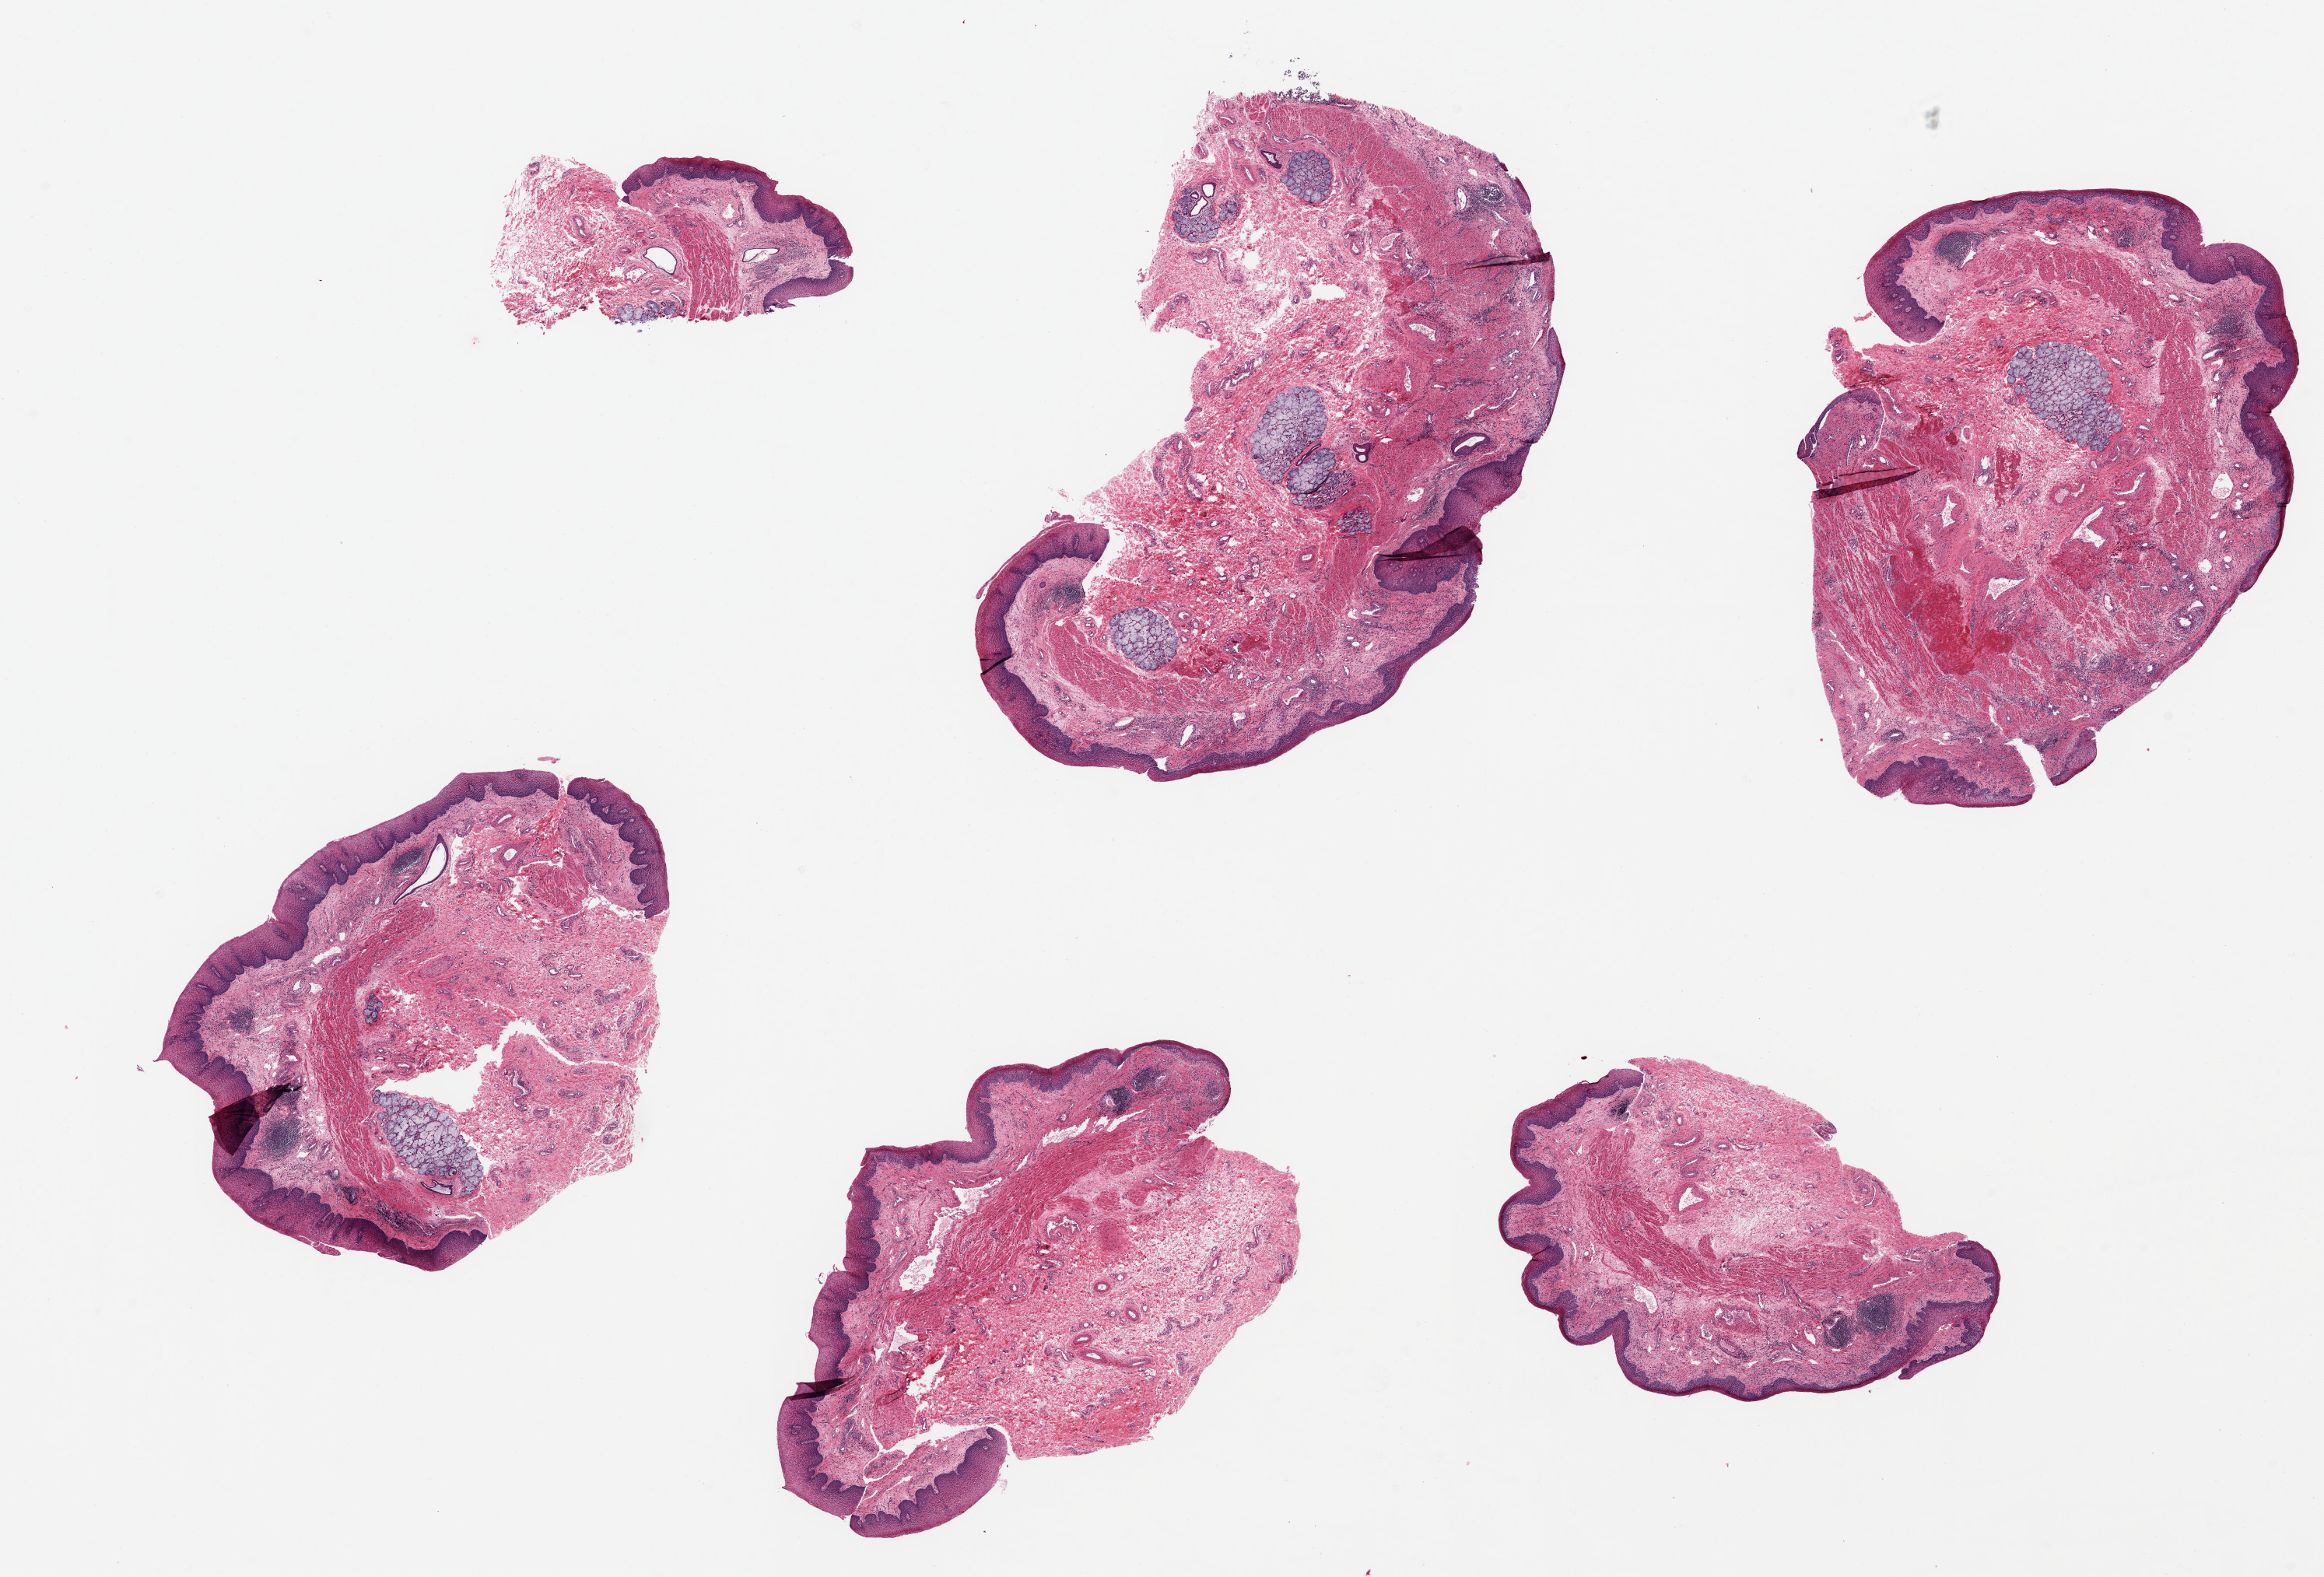
Whole-slide image, hematoxylin and eosin (H&E) stain, brightfield, low-resolution overview of the scanned area, about 23.6 x 16.0 mm; PAXgene-fixed paraffin-embedded (PFPE) section; sampled site (target tissue): esophageal mucous membrane; tissue donor sample. Male donor.
Review note (as recorded): 6 pieces up to 7x4 mm; mild chronic esophagitis with erosions.